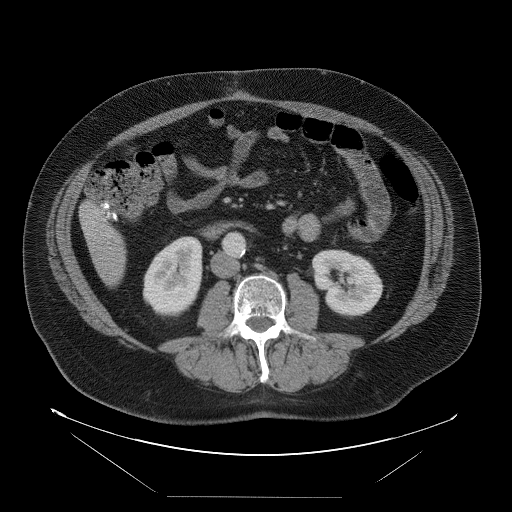
Contrast-enhanced abdominal CT, one axial slice. Slice 19 of 114 in the series (ordered by position). 120 kVp. Intravenous contrast given. Soft-tissue window (W 400 / L 40 HU). 5 mm slice thickness. 512 × 512 image matrix, field of view 500 × 500 mm. Male patient, age 61 years. Case-level facts recorded for this patient, not image findings: diagnosis: colorectal cancer liver metastases, imaged before liver resection; multiple liver metastases: no; largest metastasis: 6.5 cm; disease in both lobes: yes.
Structures marked on this image (outlined manually by an expert reader):
- liver: bounding box [x1, y1, x2, y2] px = [81, 203, 127, 286]